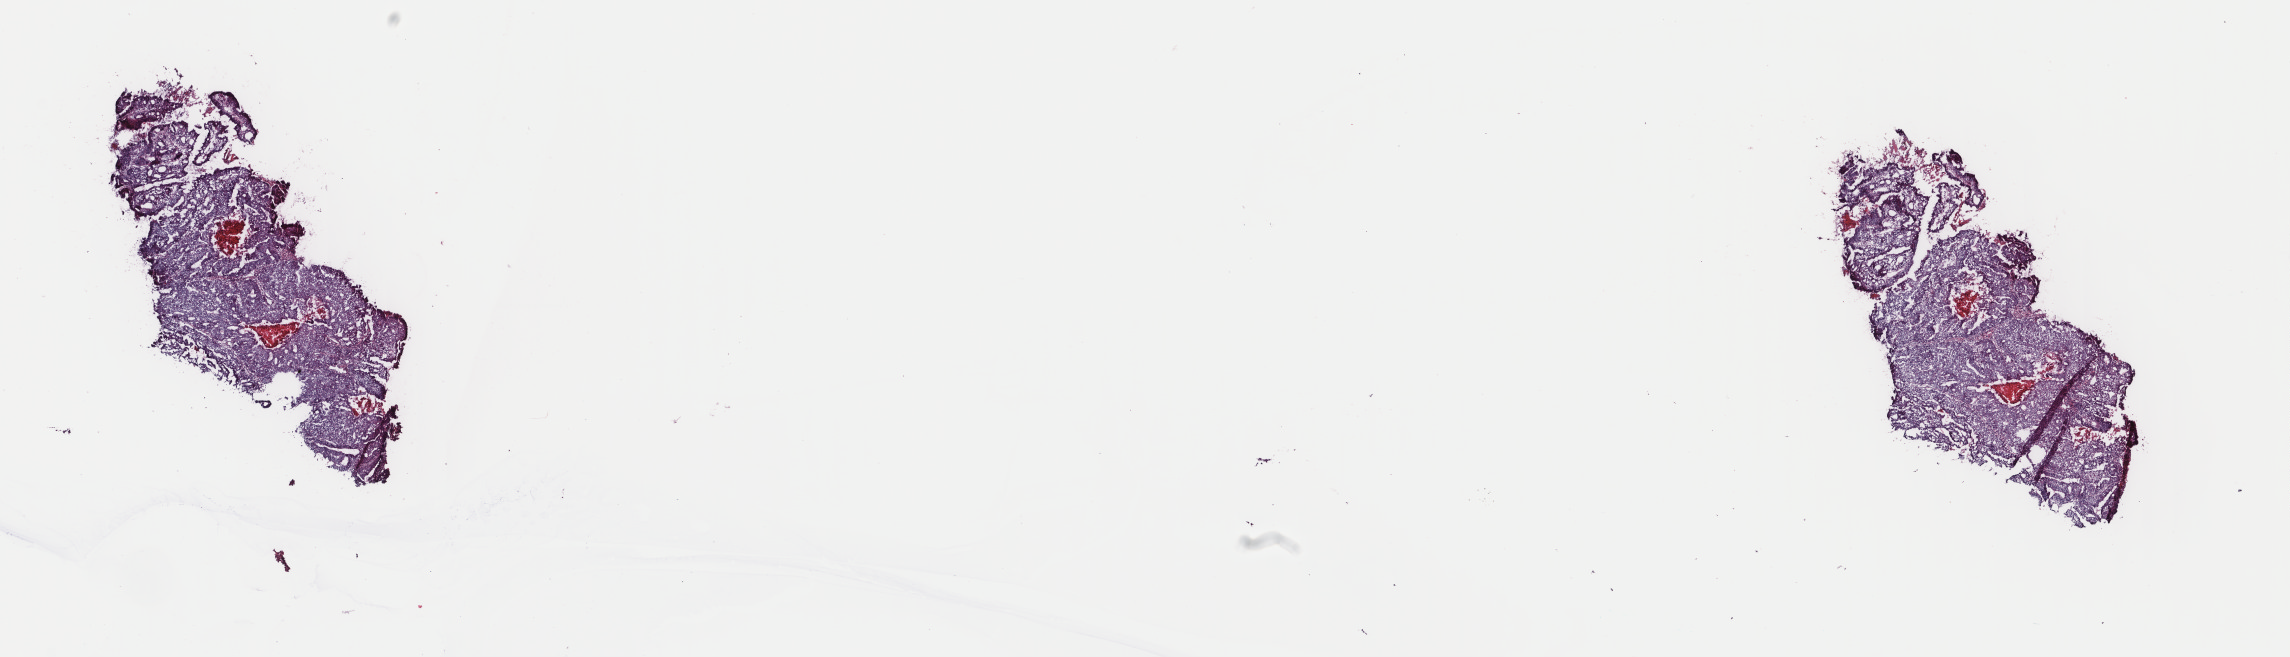
Digitized Hematoxylin and eosin (H&E) stained tissue section (whole slide), shown as a low-resolution overview of the whole scanned area (about 18.2 x 5.2 mm, acquisition: 40x scan); frozen section from the top of the tissue portion; sample: primary tumour, uterus. Female, age 77 years at initial diagnosis. Histologic grade: G3 (poorly differentiated). Slide review estimates, as recorded: tumour cells 85%, tumour nuclei 85%, normal cells 5%, stromal cells 5%, necrosis 5%. Infiltration values recorded for this section: lymphocyte infiltration 1%, monocyte infiltration 1%, neutrophil infiltration 1%.
* FIGO stage: IB
* histologic diagnosis: Endometrioid adenocarcinoma, NOS (endometrium)